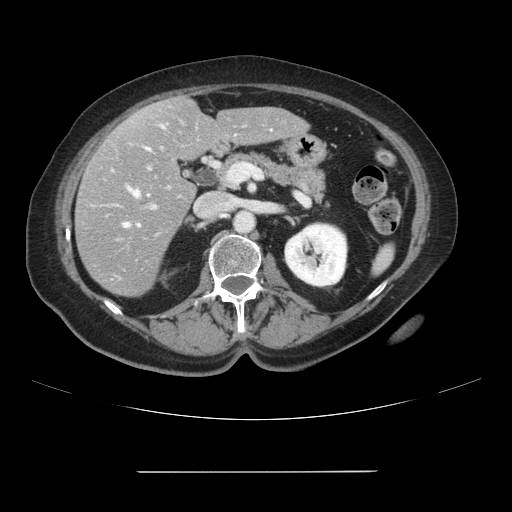
Contrast-enhanced abdominal CT, one axial slice. 120 kVp. Intravenous contrast given. Soft-tissue window (W 400 / L 40 HU). 2.5 mm slice thickness. 512 × 512 image matrix, field of view 400 × 400 mm. Female patient, age 74 years. From the clinical record (not read from this slice): diagnosis: colorectal cancer liver metastases, imaged before liver resection; multiple liver metastases: yes; largest metastasis: 1.1 cm; chemotherapy before resection: yes.
Structures marked on this image (manually delineated by an expert):
- hepatic veins: box from (x=124, y=126) to (x=163, y=228) px
- liver: (x=75, y=97)–(x=308, y=297)
- planned liver remnant (the part of the liver to remain after resection): (x=141, y=97)–(x=308, y=161)
- portal vein (with intrahepatic branches): (x=152, y=206)–(x=155, y=208)